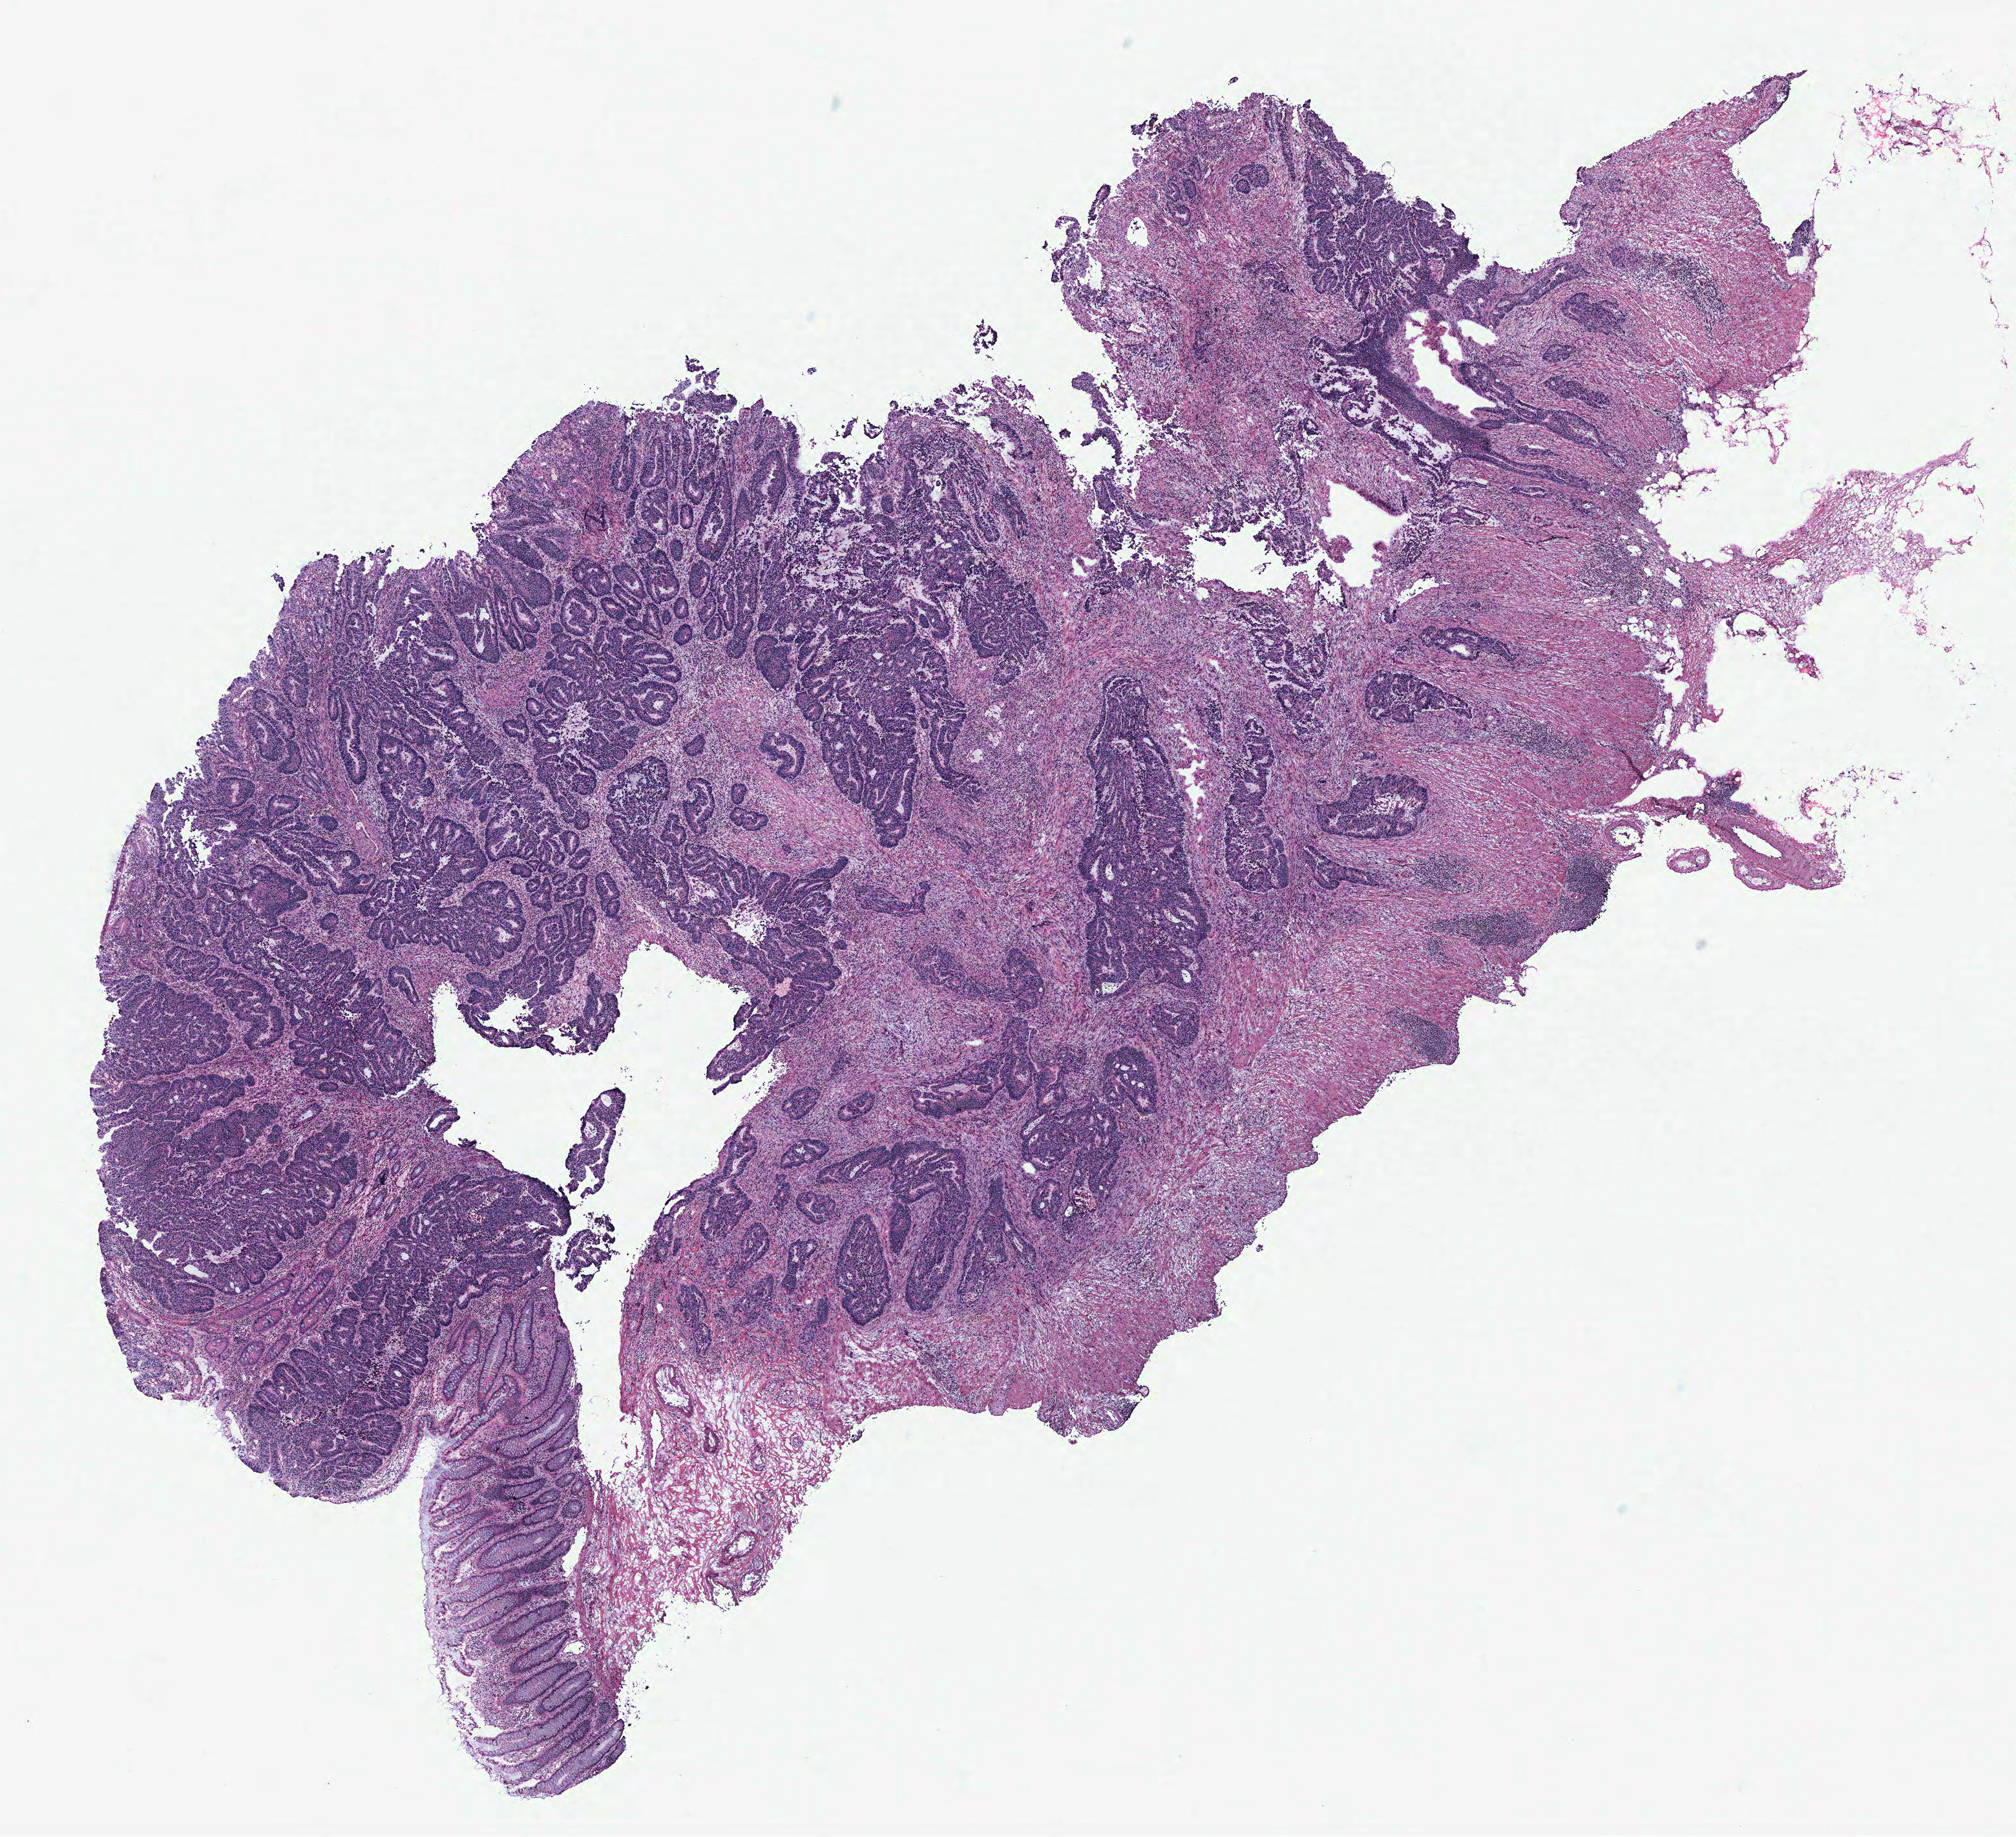
Whole-slide histology image, H&E-stained — shown as a low-resolution overview of the whole scanned area (about 12.5 x 11.4 mm, slide scanned at 40x); normal (non-tumour) tissue sample, colon. 53-year-old female patient.
This section: normal (non-tumour) tissue from the same patient. Patient diagnosis: Adenocarcinoma, NOS.